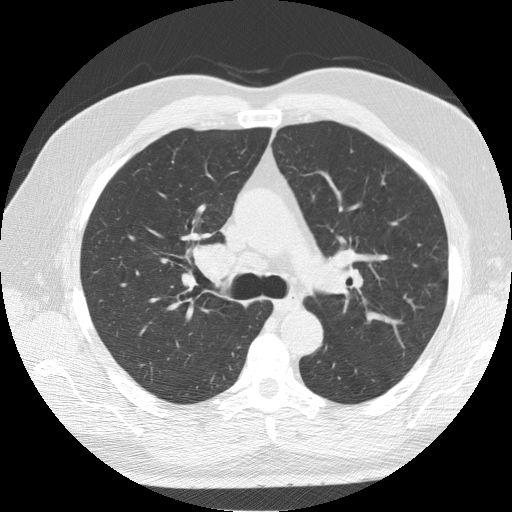
Low-dose screening chest CT, one axial slice; slice 94 of 139 in the series (ordered by position); 120 kVp; lung window (W 1500 / L -600 HU); 2.5 mm slice thickness; 512 × 512 image matrix.
Annotated regions visible in this slice (expert manual segmentation):
- lesion 1 (tumor, upper lobe of right lung): bounding box <194,244,235,280> (left, top, right, bottom; pixels)